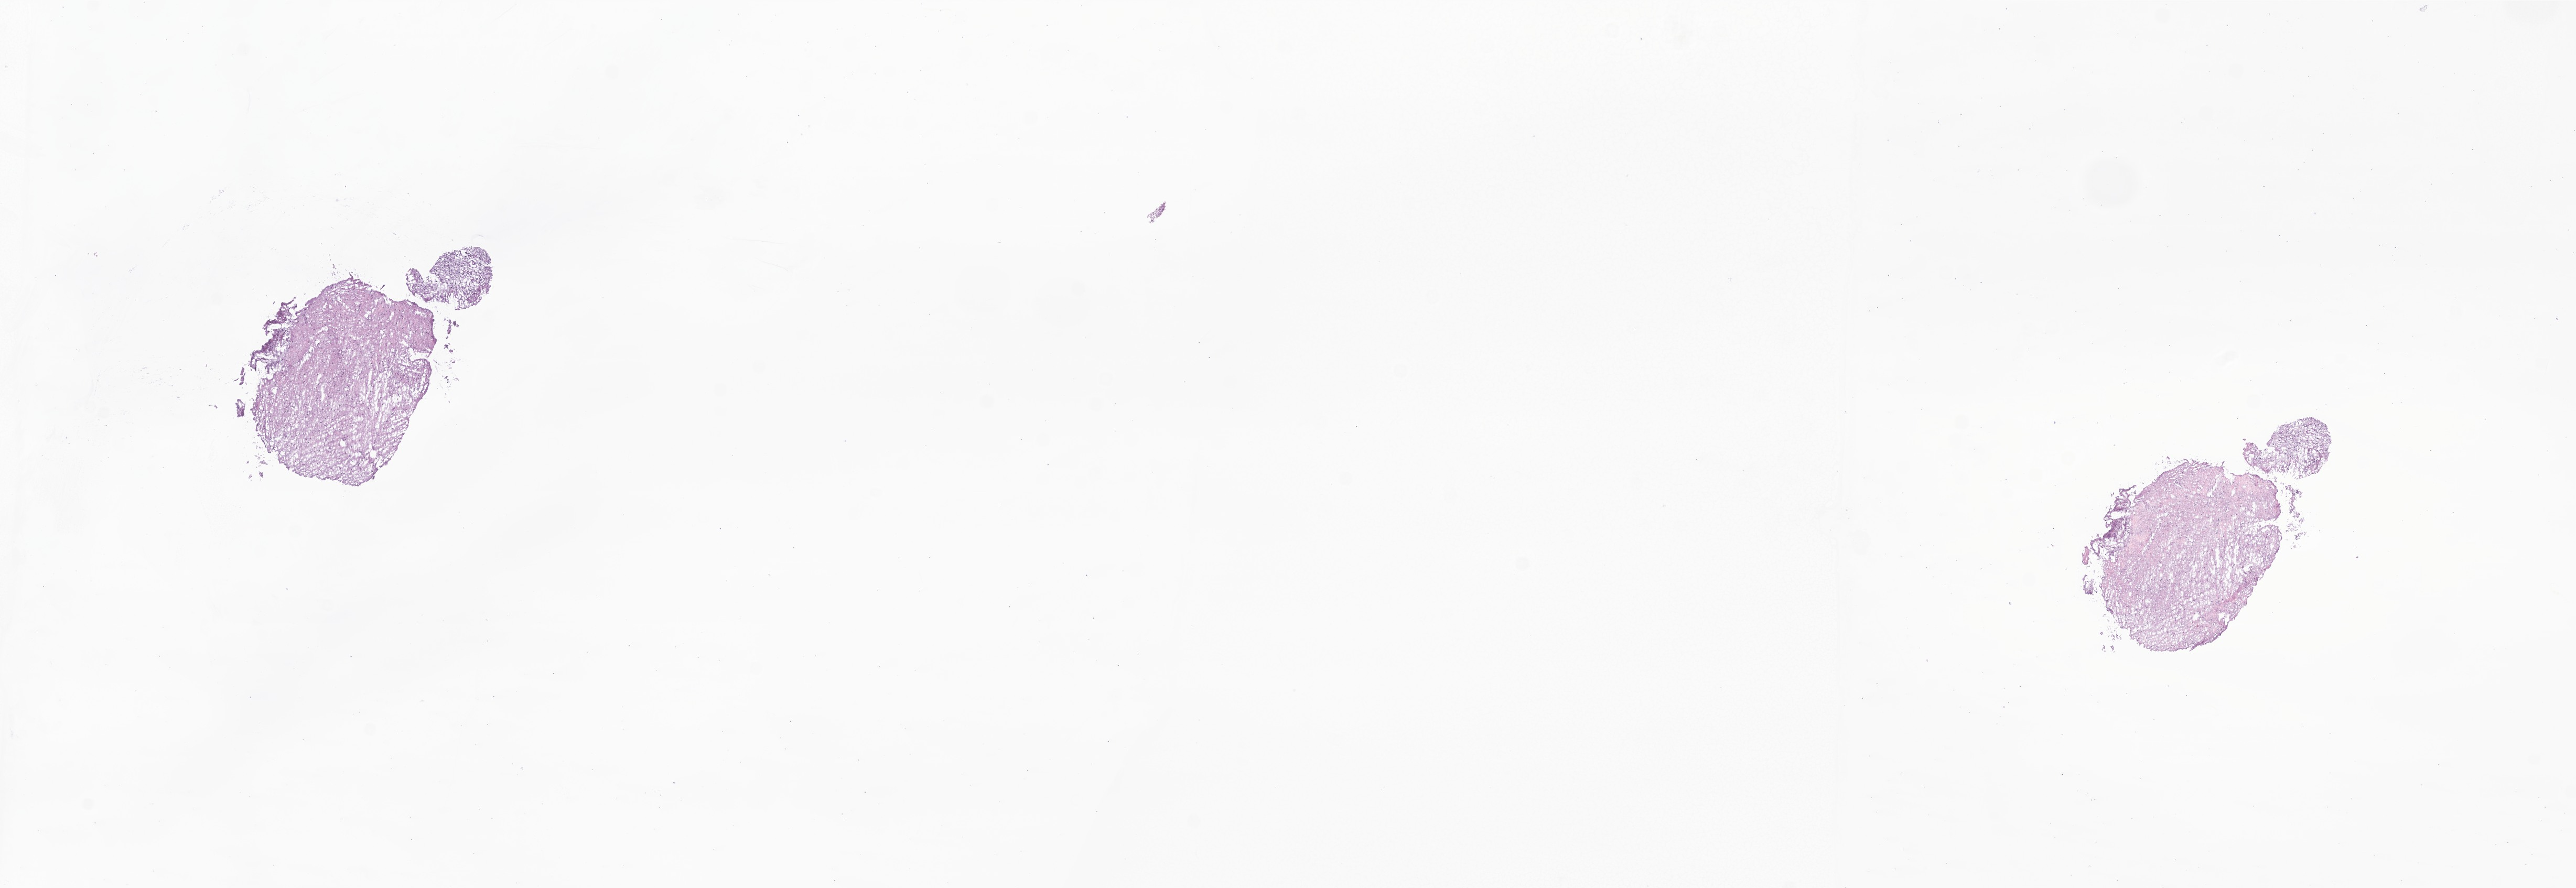
Whole-slide image, hematoxylin and eosin (H&E) stain of tumor tissue from the brain — low-resolution overview of the scanned area, about 20.7 x 7.1 mm, cryosection (OCT / tissue freezing medium). Patient: female, age 233 months (19 years 5 months).
Recorded diagnosis: Pilocytic astrocytoma.